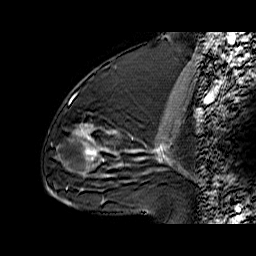
Breast MRI (dynamic contrast-enhanced), one sagittal slice; slice 33 of 60 in the series (ordered by position); dynamic contrast-enhanced series, time point 2 of 6 at this slice position (early post-contrast); 1.5 T; TE 6.3 ms, TR 32.9 ms; 256 × 256 image matrix. Female patient. From the clinical record (not read from this slice): setting: breast cancer imaged before/during neoadjuvant chemotherapy; receptor status: triple-negative.
Outlined on this slice (semi-automatic segmentation, software-assisted and operator-edited):
- analysis volume of interest (the breast-tissue region the enhancement analysis was run in; not a lesion): bounding box [x1, y1, x2, y2] px = [55, 76, 131, 170]
- tumour enhancement mask (voxels above the 100 % enhancement threshold inside the analysis volume of interest): [75, 124, 120, 166]